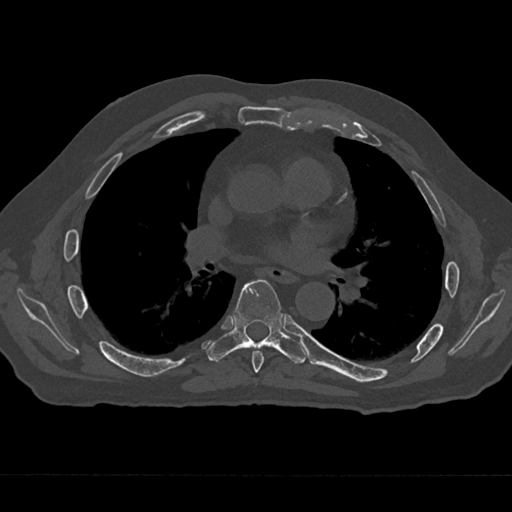
CT including the spine, one axial slice; slice 388 of 797 in the series (ordered by position); 120 kVp; bone window (W 1800 / L 400 HU); 512 × 512 image matrix, field of view 377 × 377 mm. Patient: male, 75 years. Case-level facts recorded for this patient, not image findings: primary cancer: renal; vertebrae with lytic lesions (as recorded): T4.
Annotated regions visible in this slice (semi-automatic segmentation, software-assisted and operator-edited):
- T6 vertebra: bounding box <252,351,264,373> (left, top, right, bottom; pixels)
- T7 vertebra: <207,279,306,364>